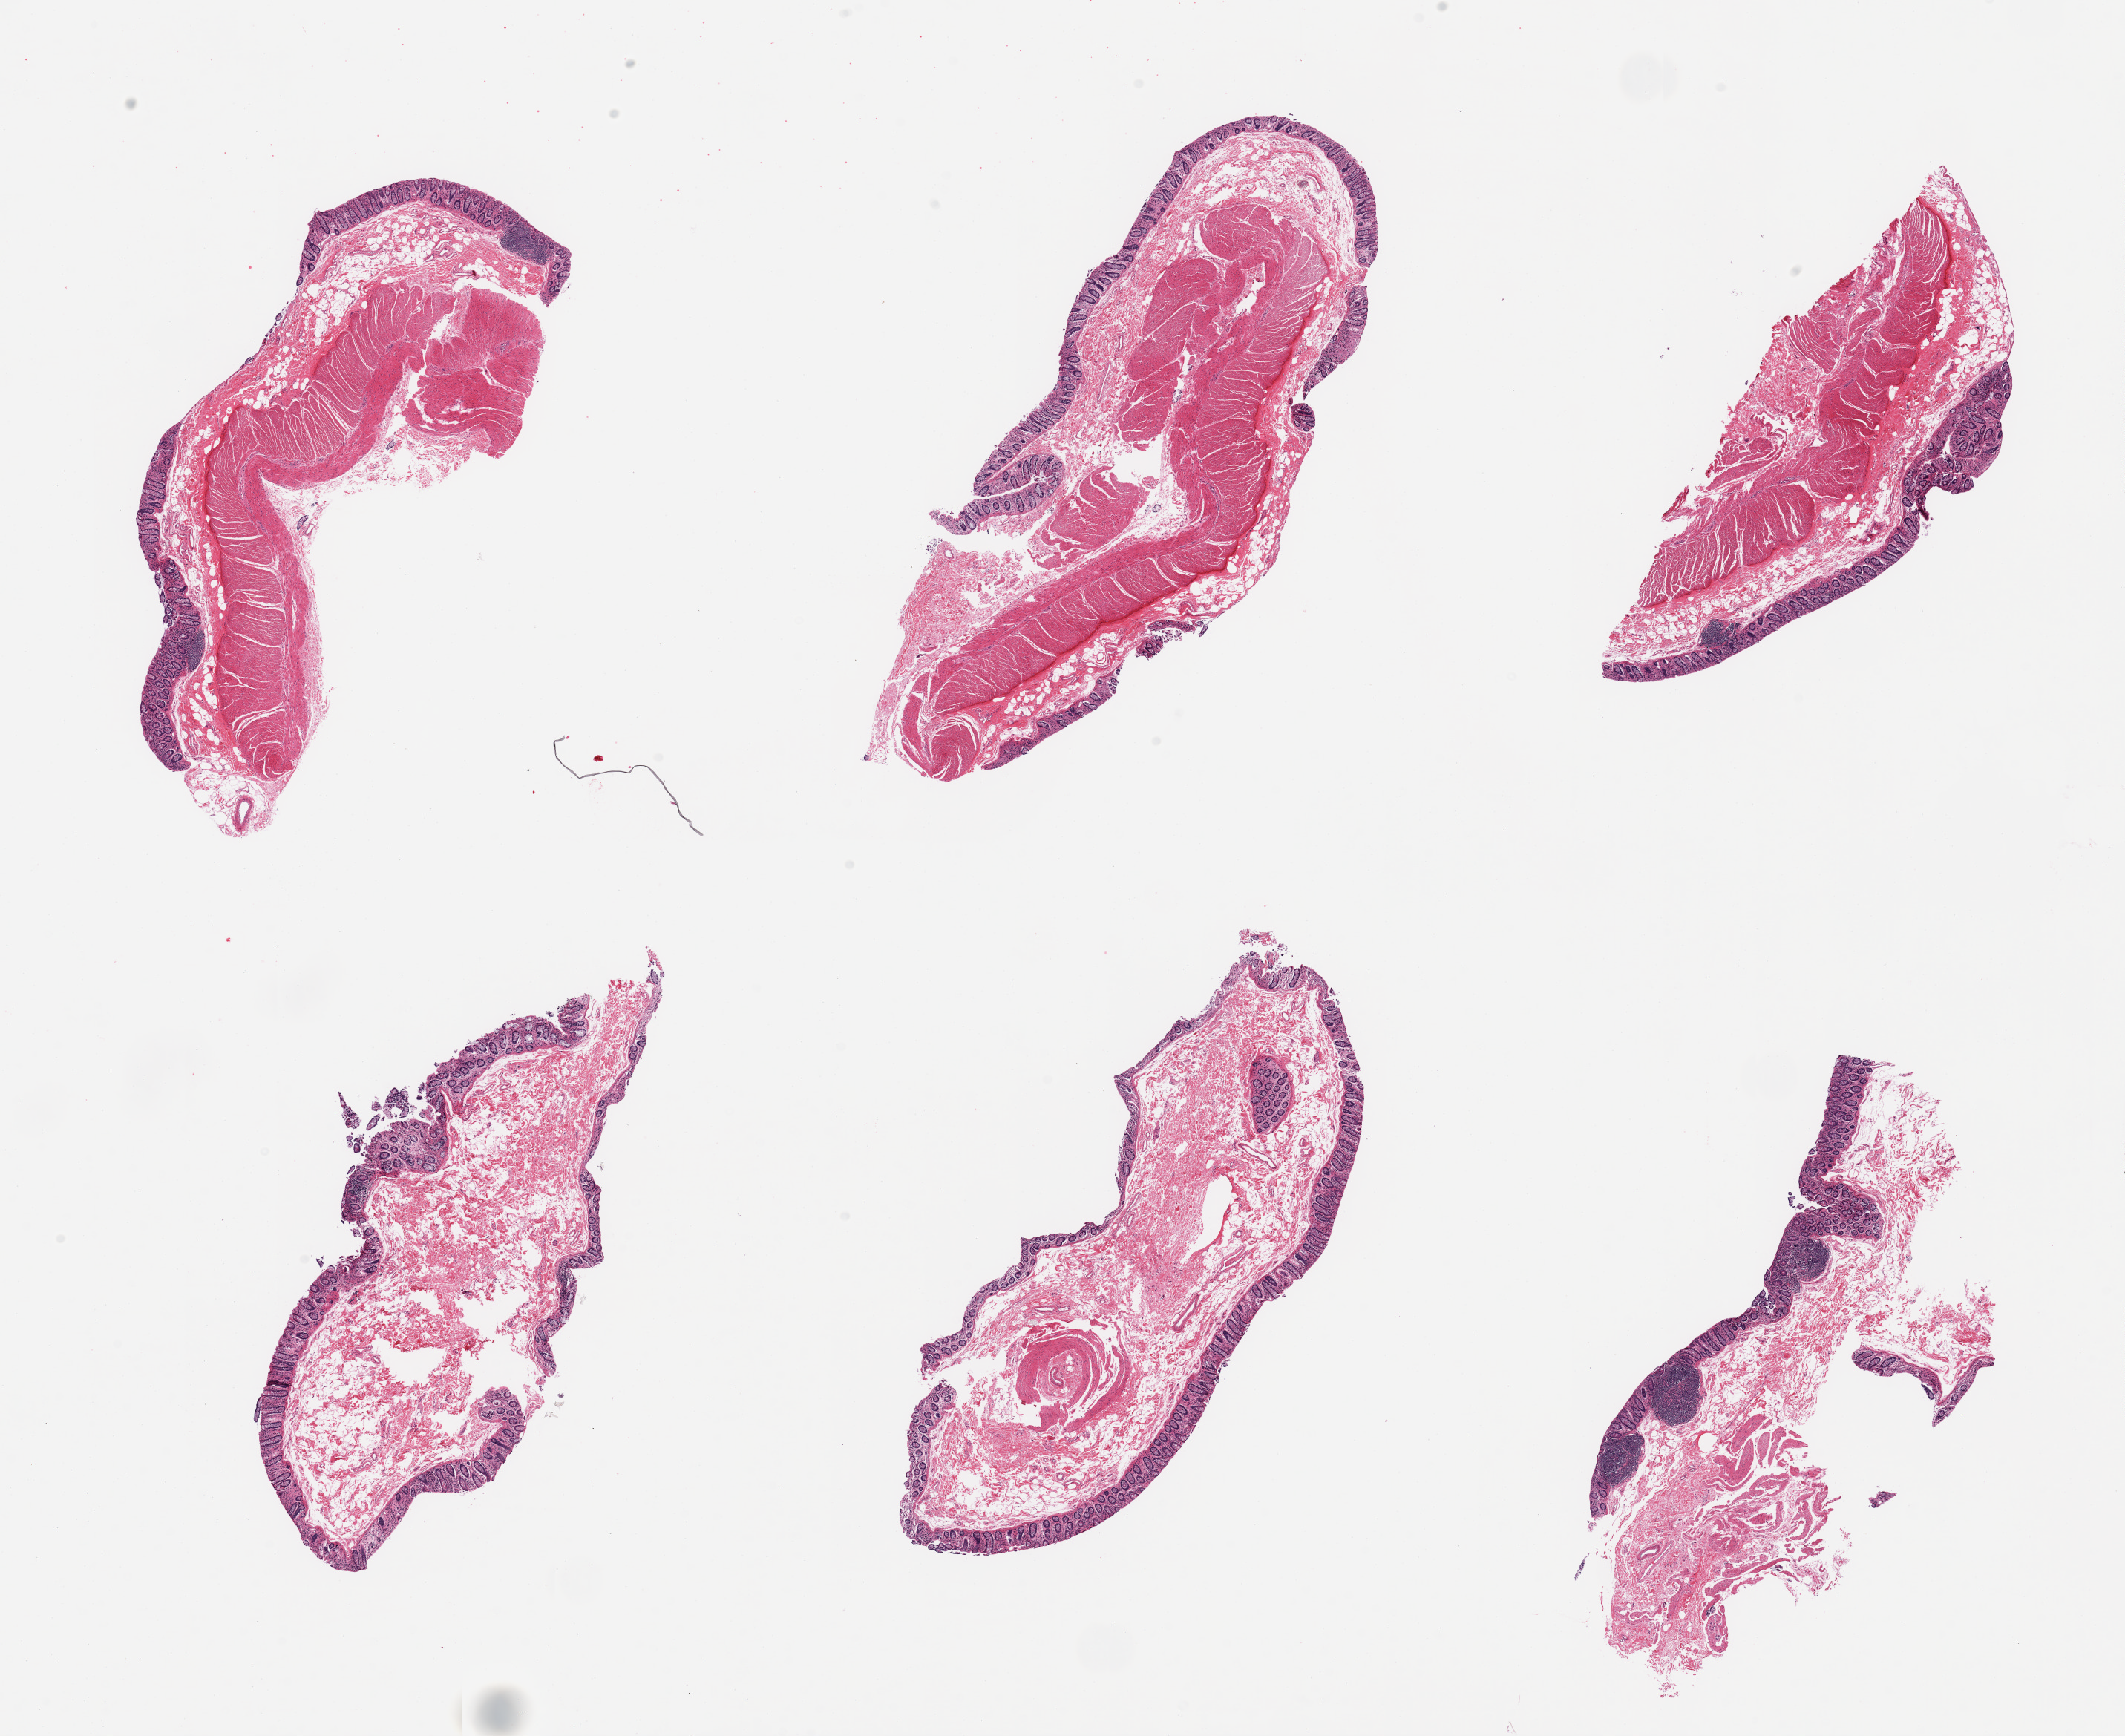
Whole-slide image, H&E stain — a low-resolution overview of the entire scanned area, about 22.6 x 18.5 mm, PAXgene-fixed paraffin-embedded (PFPE) section, section of transverse colon (target tissue), tissue donor sample. Donor sex: male.
Review note (as recorded): 6 pieces, mucosa up to ~0.3mm, 10-20% thickness.